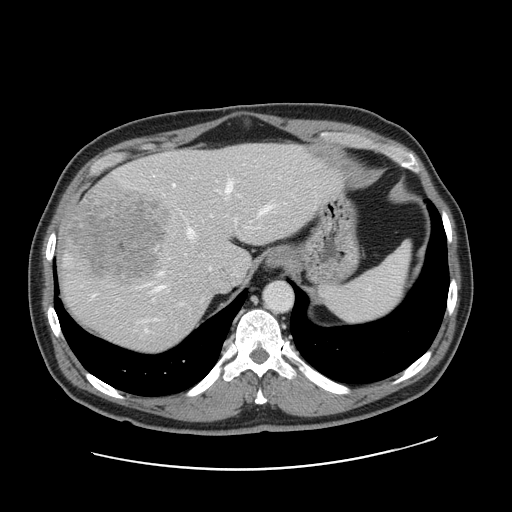
Contrast-enhanced abdominal CT, one axial slice. Position 125 of 178 along the scan axis. Intravenous contrast given. Soft-tissue window (W 400 / L 40 HU). 2.5 mm slice thickness. 512 × 512 image matrix, field of view 403 × 403 mm. Male patient, age 63 years. From the clinical record (not read from this slice): diagnosis: colorectal cancer liver metastases, imaged before liver resection; multiple liver metastases: yes; largest metastasis: 8 cm; disease in both lobes: yes.
Structures marked on this image (outlined manually by an expert reader):
- hepatic veins: bounding box [x1, y1, x2, y2] px = [155, 181, 270, 290]
- liver: [60, 143, 340, 351]
- planned liver remnant (the part of the liver to remain after resection): [147, 144, 341, 280]
- portal vein (with intrahepatic branches): [155, 184, 213, 320]
- liver metastasis: [67, 191, 170, 280]